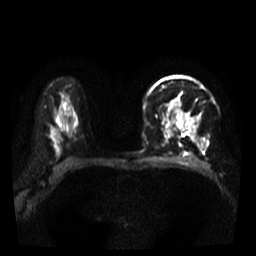
Breast MRI, one axial slice. Slice 26 of 39 in the series (ordered by position). Diffusion-weighted series; image 2 of 4 stored at this slice position (different b-values; order by instance number). 3 T. 5 mm slice thickness. 256 × 256 image matrix, field of view 320 × 320 mm. Female patient.
Structures marked on this image (expert manual segmentation):
- tumour on diffusion-weighted imaging: bounding box [x1, y1, x2, y2] px = [194, 117, 198, 122]